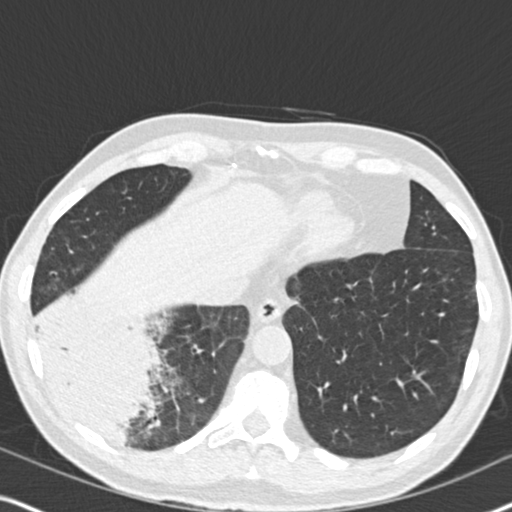
Axial slice from a low-dose chest CT screening exam; second annual screen; lung window (W 1500 / L -600 HU); 2 mm slice thickness; 512 × 512 image matrix. Male, age 61 years at enrolment.
- Expert reader's lesion annotation, bounding box <26,290,182,457> (left, top, right, bottom; pixels).
- Screening reader's record for this exam (one nodule recorded; not confirmed to be the boxed lesion): non-calcified nodule or mass ≥4 mm, right lower lobe, 90 × 80 mm, soft tissue attenuation, pre-existing on the prior screen: yes; interval growth: yes.
- Official screen result: positive, other.